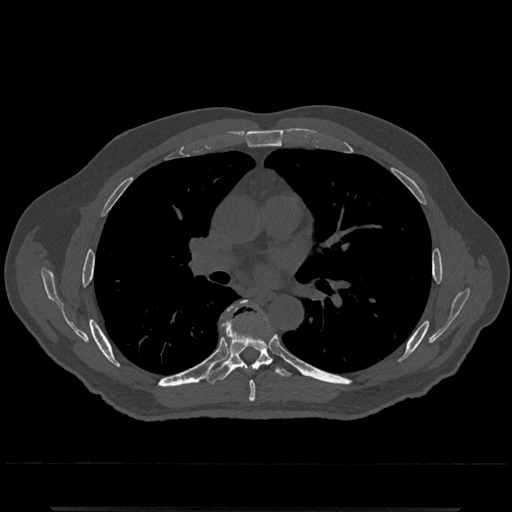
CT including the spine, one axial slice. Slice 742 of 797 in the series (ordered by position). Reconstruction kernel Br40s/3. 120 kVp. Bone window (W 1800 / L 400 HU). 0.5 mm slice thickness. 512 × 512 image matrix, field of view 393 × 393 mm. Male patient, age 67 years. From the clinical record (not read from this slice): primary cancer: prostate.
Structures marked on this image (semi-automatically segmented with operator editing):
- T6 vertebra: bounding box <243,301,256,402> (left, top, right, bottom; pixels)
- T7 vertebra: <203,302,293,385>